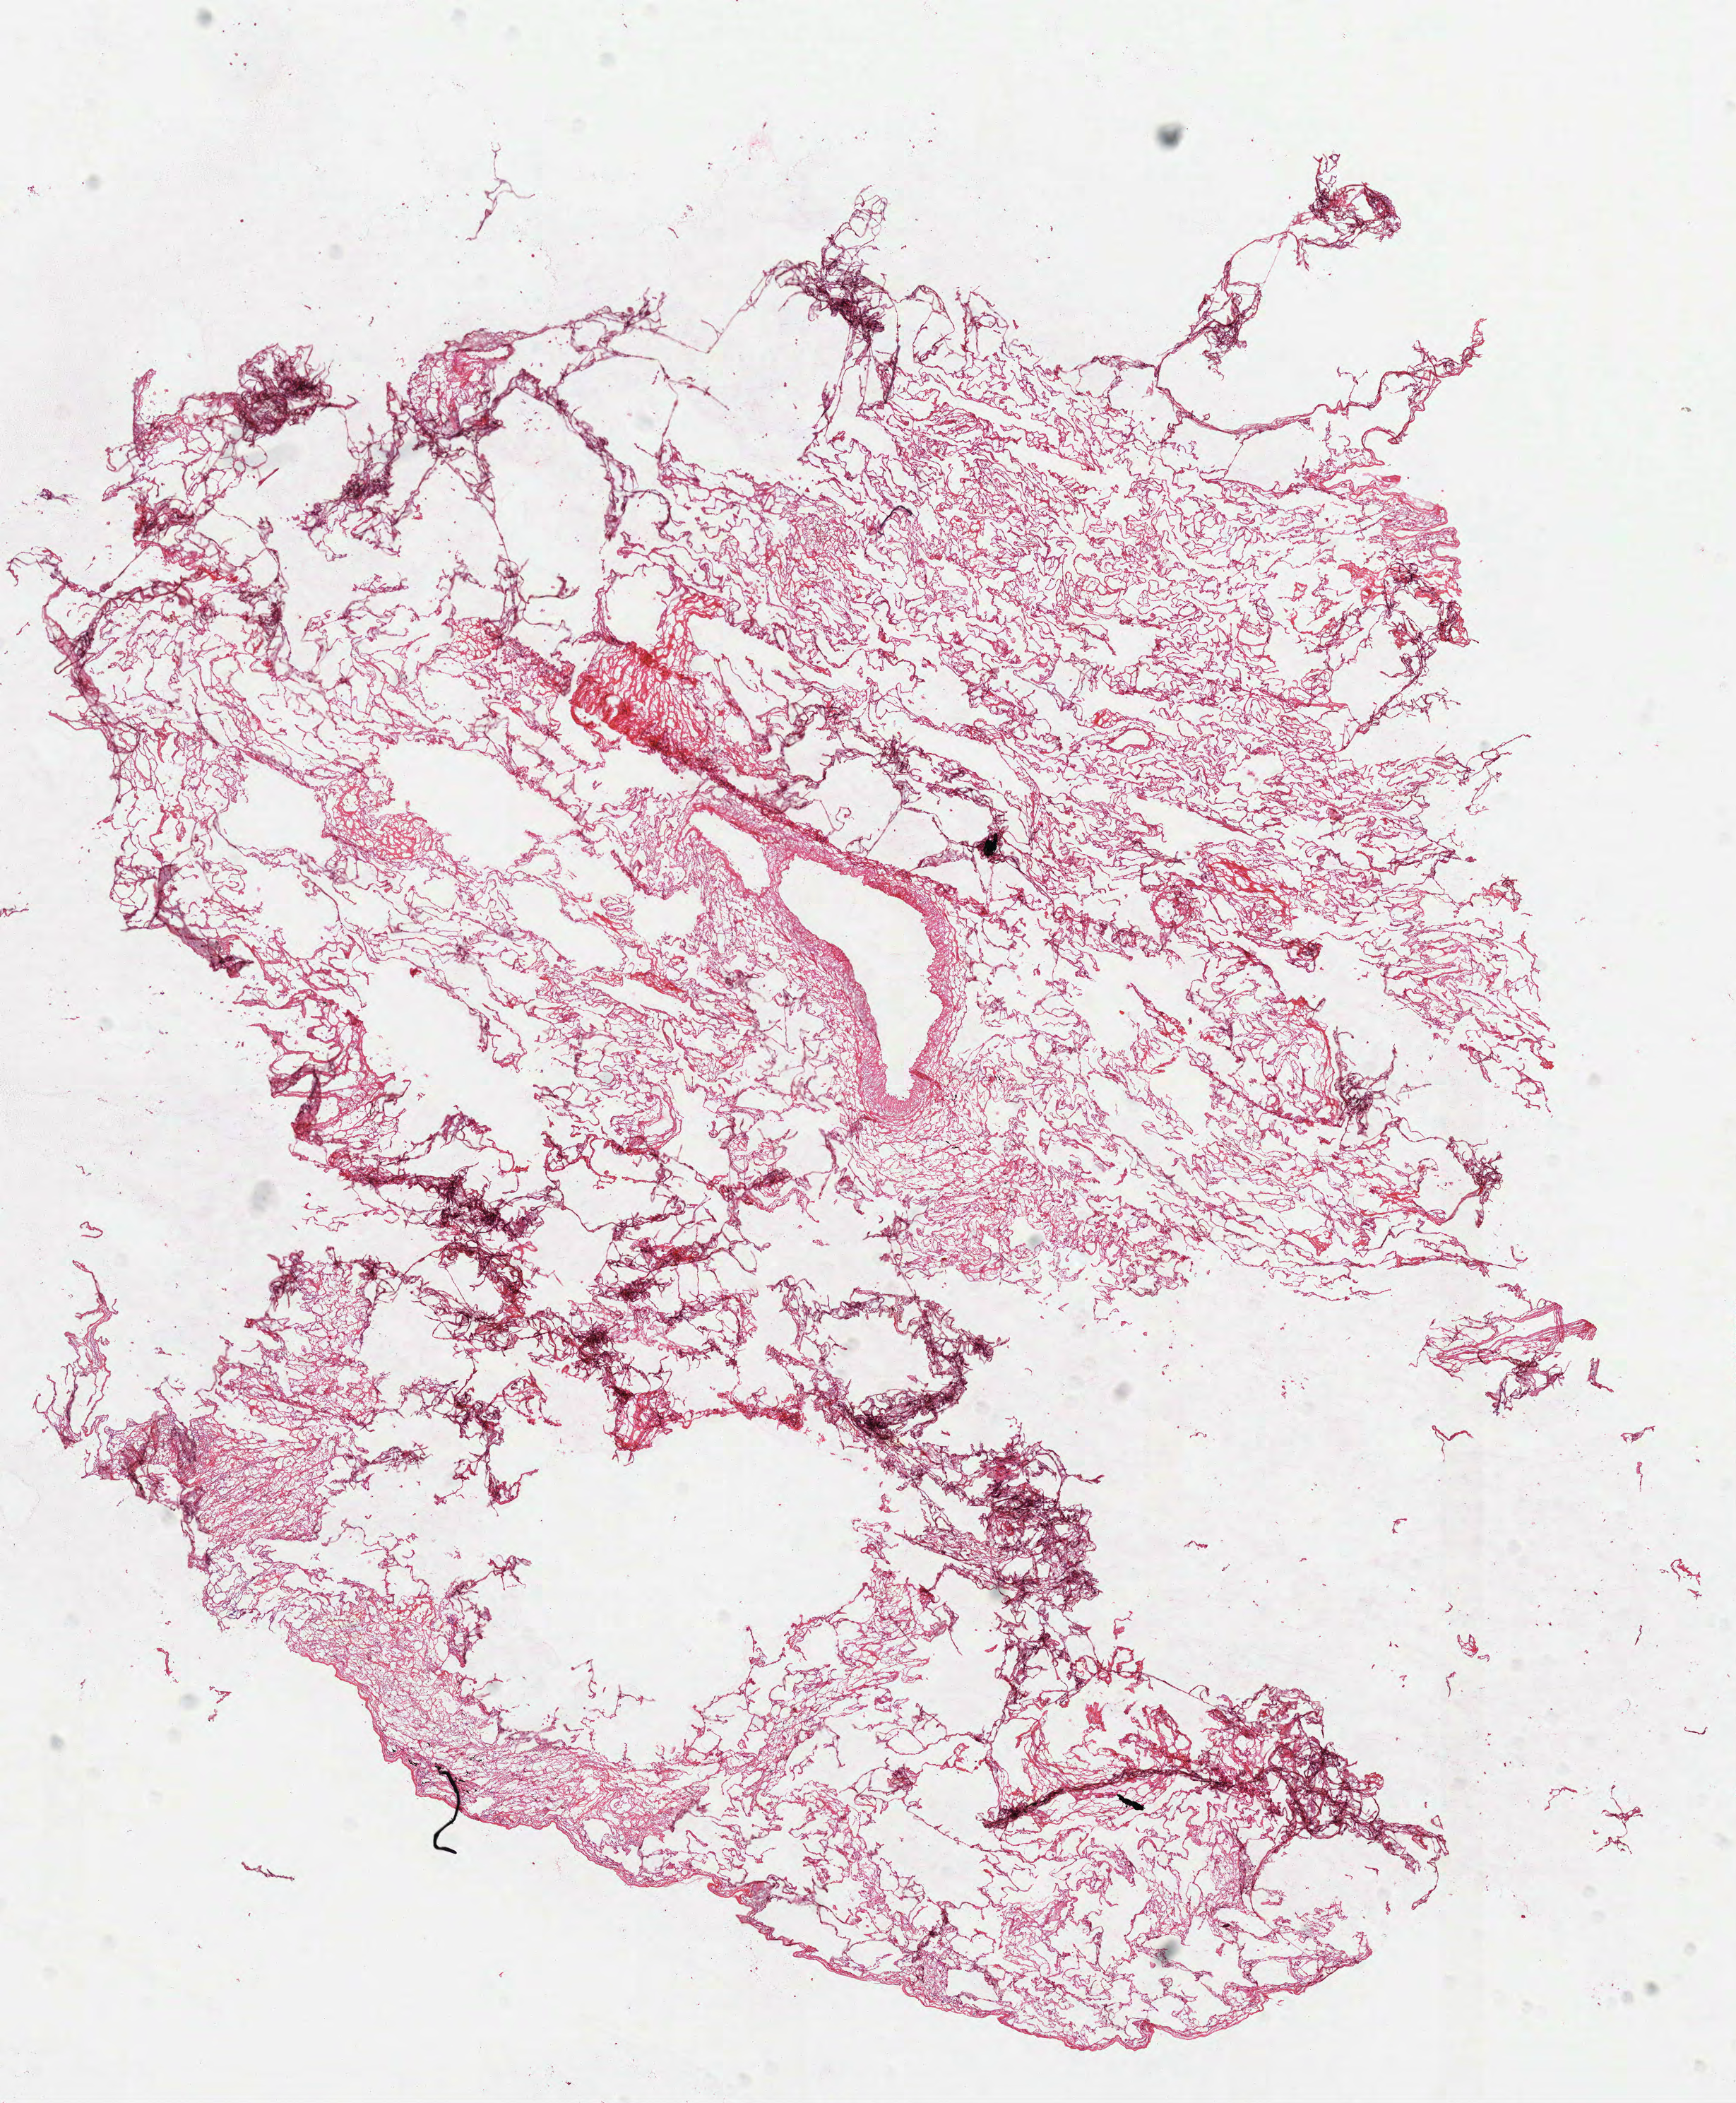
Whole-slide histology image, H&E-stained, whole scanned area (about 9.9 x 12.0 mm) shown as a low-resolution overview; frozen section from the top of the tissue portion; lung, solid tissue normal (non-tumour tissue) sample. Female, age 71 years at initial diagnosis.
This section: solid tissue normal (non-tumour) sample from the same patient. Patient diagnosis: Squamous cell carcinoma, NOS.